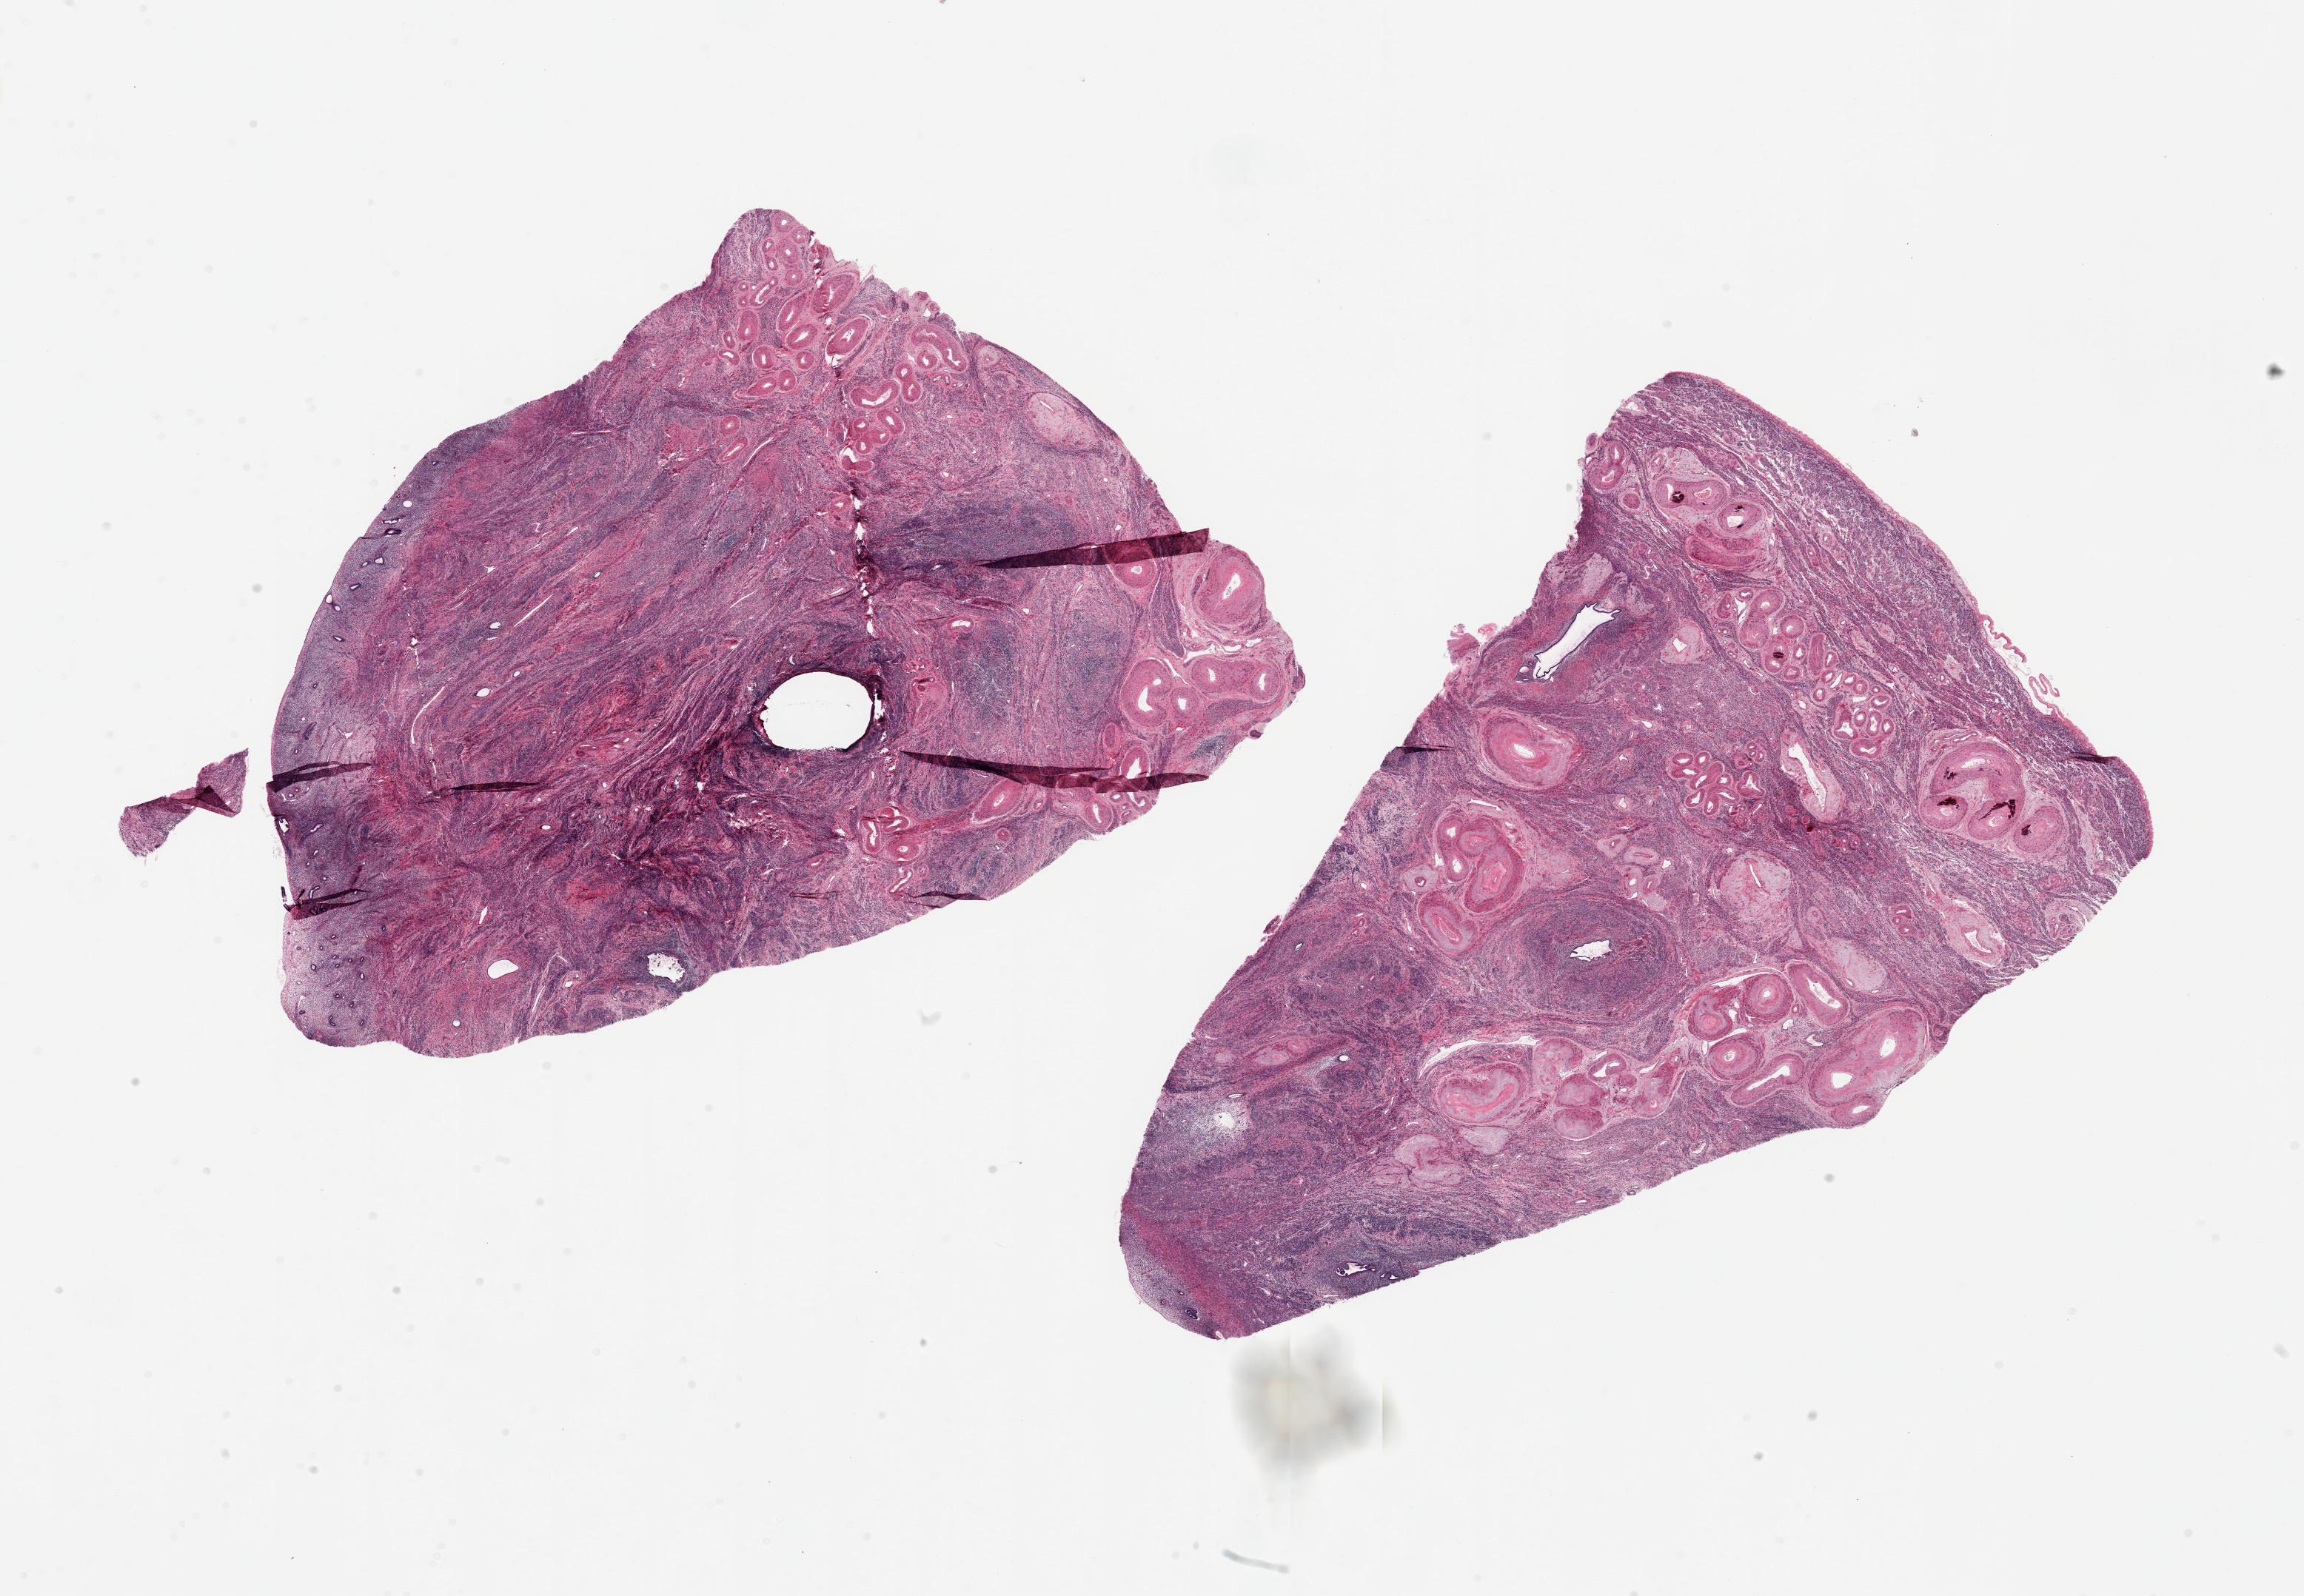
Whole-slide image, H&E stain — low-resolution overview of the scanned area, about 24.6 x 17.1 mm (acquisition: 20x scan); PAXgene-fixed, paraffin-embedded tissue; target tissue: uterus; tissue donor sample. Donor sex: female.
* reviewer comment on this tissue sample: 2 pieces; 10% atrophic endometrium, remainder myometrium